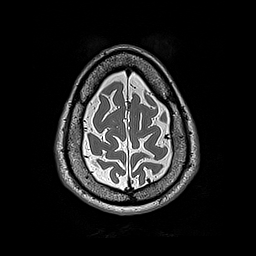
Brain MRI from a brain-tumour surgery series, one axial slice; position 50 of 192 along the scan axis; 1 mm slice thickness; 256 × 256 image matrix. From the clinical record (not read from this slice): histopathology: Astrocytoma; WHO grade: 2; IDH mutation: yes; tumour location: Left Frontal.
Structures marked on this image (outlined manually by an expert reader):
- tumour: box from (x=162, y=117) to (x=164, y=119) px